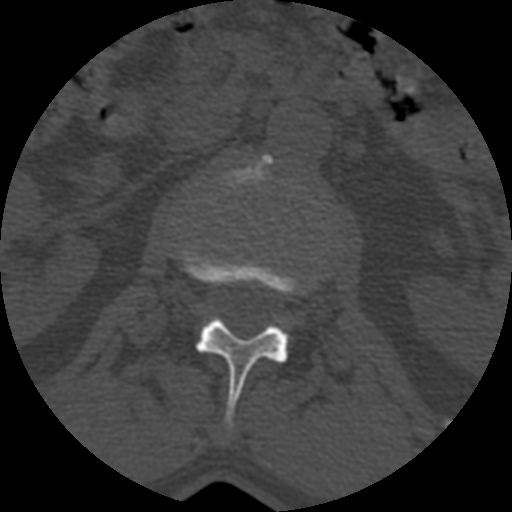
CT including the spine, one axial slice. Position 353 of 399 along the scan axis. 120 kVp. Bone window (W 1800 / L 400 HU). 512 × 512 image matrix, field of view 160 × 160 mm. Patient age 71 years. From the clinical record (not read from this slice): primary cancer: prostate.
Outlined on this slice (semi-automatic segmentation, software-assisted and operator-edited):
- L1 vertebra: bounding box (x1, y1, x2, y2) in pixels: (178, 243, 300, 428)
- L2 vertebra: (220, 155, 279, 187)